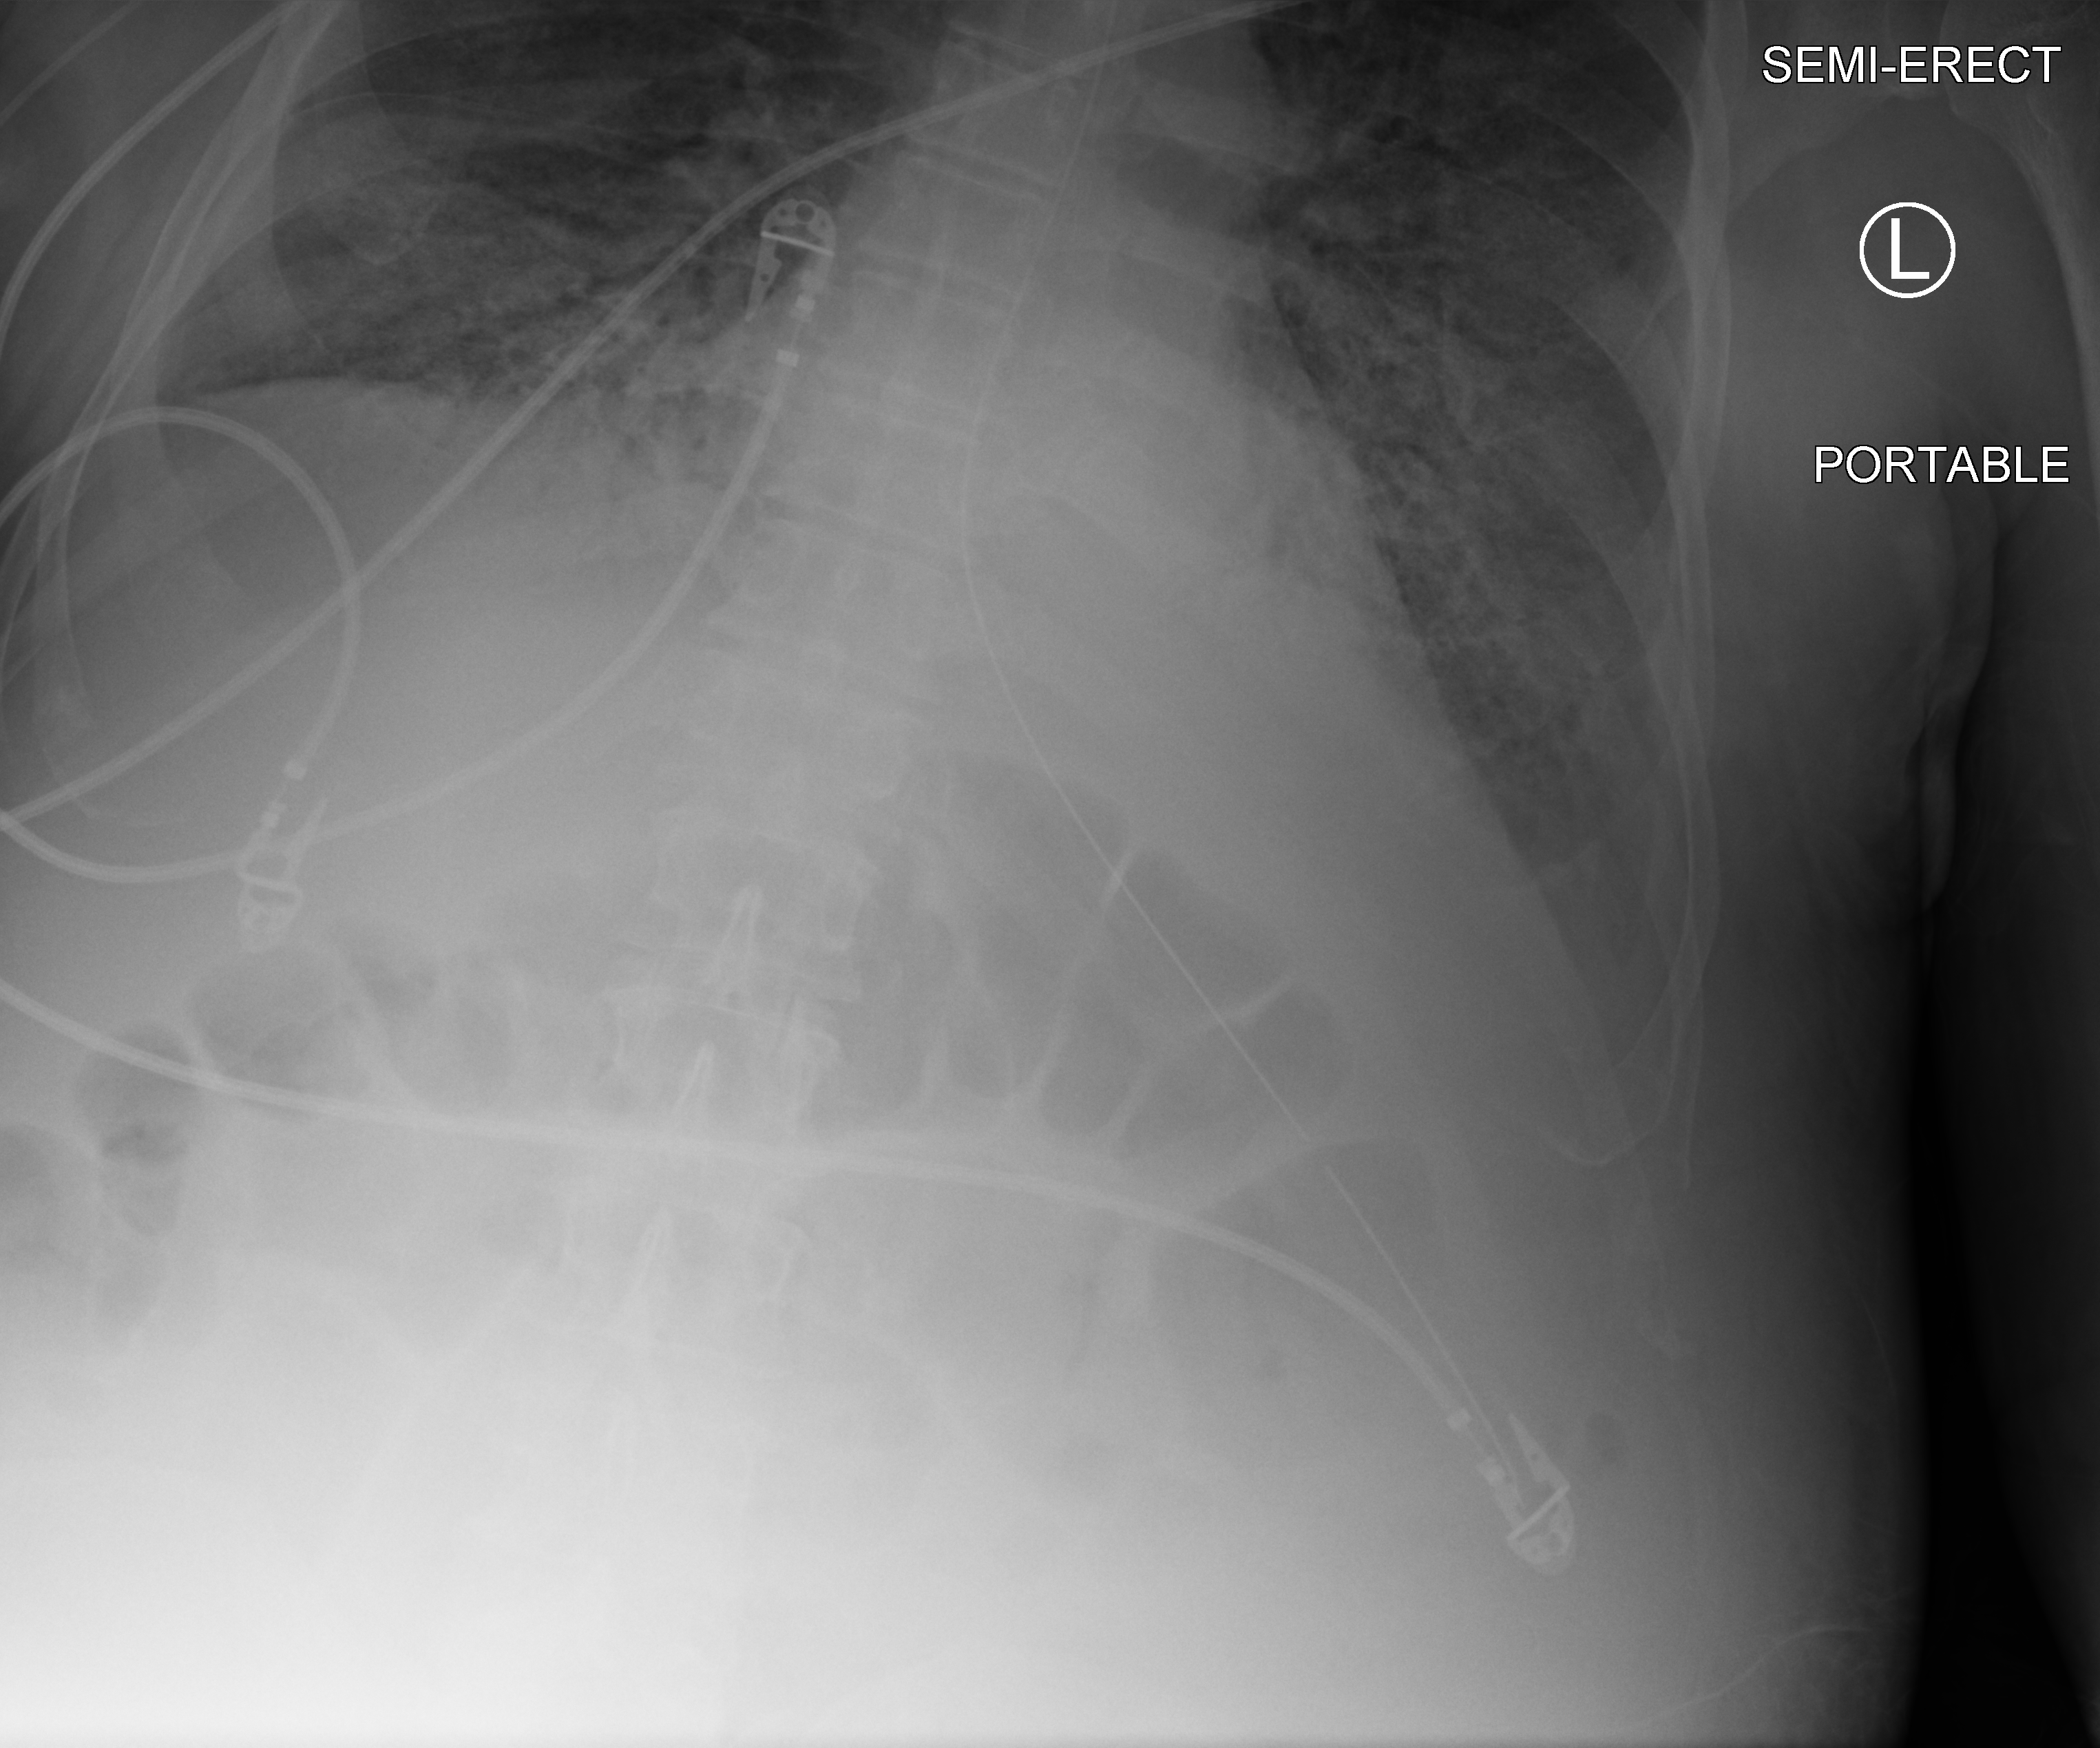
Chest X-ray (portable); anteroposterior (AP) projection. Male patient hospitalised with COVID-19, age 60–74 years.
Admission-level facts for this patient (not findings on this image; timing relative to this image not recorded):
- COPD (admission record): no
- admitted to intensive care during this hospital stay: yes
- length of hospital stay: 24 days